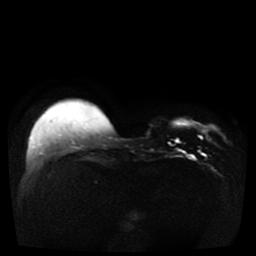
Breast MRI, one axial slice. Position 8 of 41 along the scan axis. Diffusion-weighted series; image 2 of 4 stored at this slice position (different b-values; order by instance number). 1.5 T. 5 mm slice thickness. 256 × 256 image matrix. Female patient.
Annotated regions visible in this slice (expert manual segmentation):
- tumour on diffusion-weighted imaging: bounding box <200,136,203,140> (left, top, right, bottom; pixels)